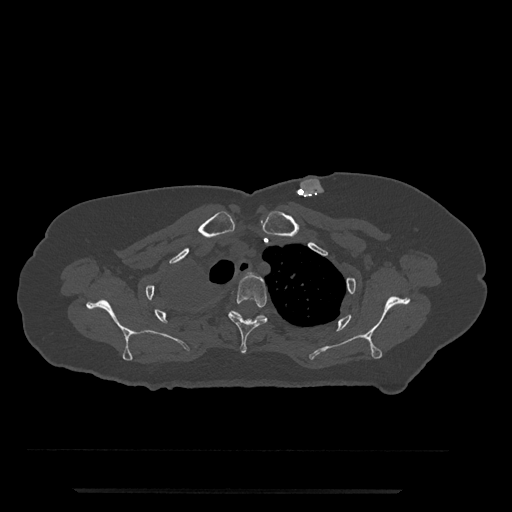
CT including the spine, one axial slice. Position 626 of 797 along the scan axis. Reconstruction kernel Br40s/3. Bone window (W 1800 / L 400 HU). 512 × 512 image matrix, field of view 440 × 440 mm. Female patient, age 51 years. From the clinical record (not read from this slice): primary cancer: neuro; vertebrae with lytic lesions (as recorded): T8.
Outlined on this slice (semi-automatically segmented with operator editing):
- T3 vertebra: bounding box <228,273,268,354> (left, top, right, bottom; pixels)
- T4 vertebra: <231,310,266,319>